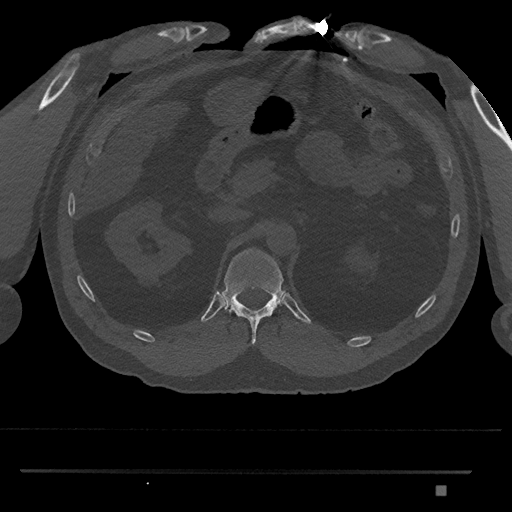
CT including the spine, one axial slice; position 883 of 1134 along the scan axis; reconstruction kernel Br40s/3; 120 kVp; bone window (W 1800 / L 400 HU); 512 × 512 image matrix, field of view 429 × 429 mm. Male patient, age 65 years. From the clinical record (not read from this slice): primary cancer: prostate.
Structures marked on this image (semi-automatically segmented with operator editing):
- T12 vertebra: bounding box <219,248,285,346> (left, top, right, bottom; pixels)